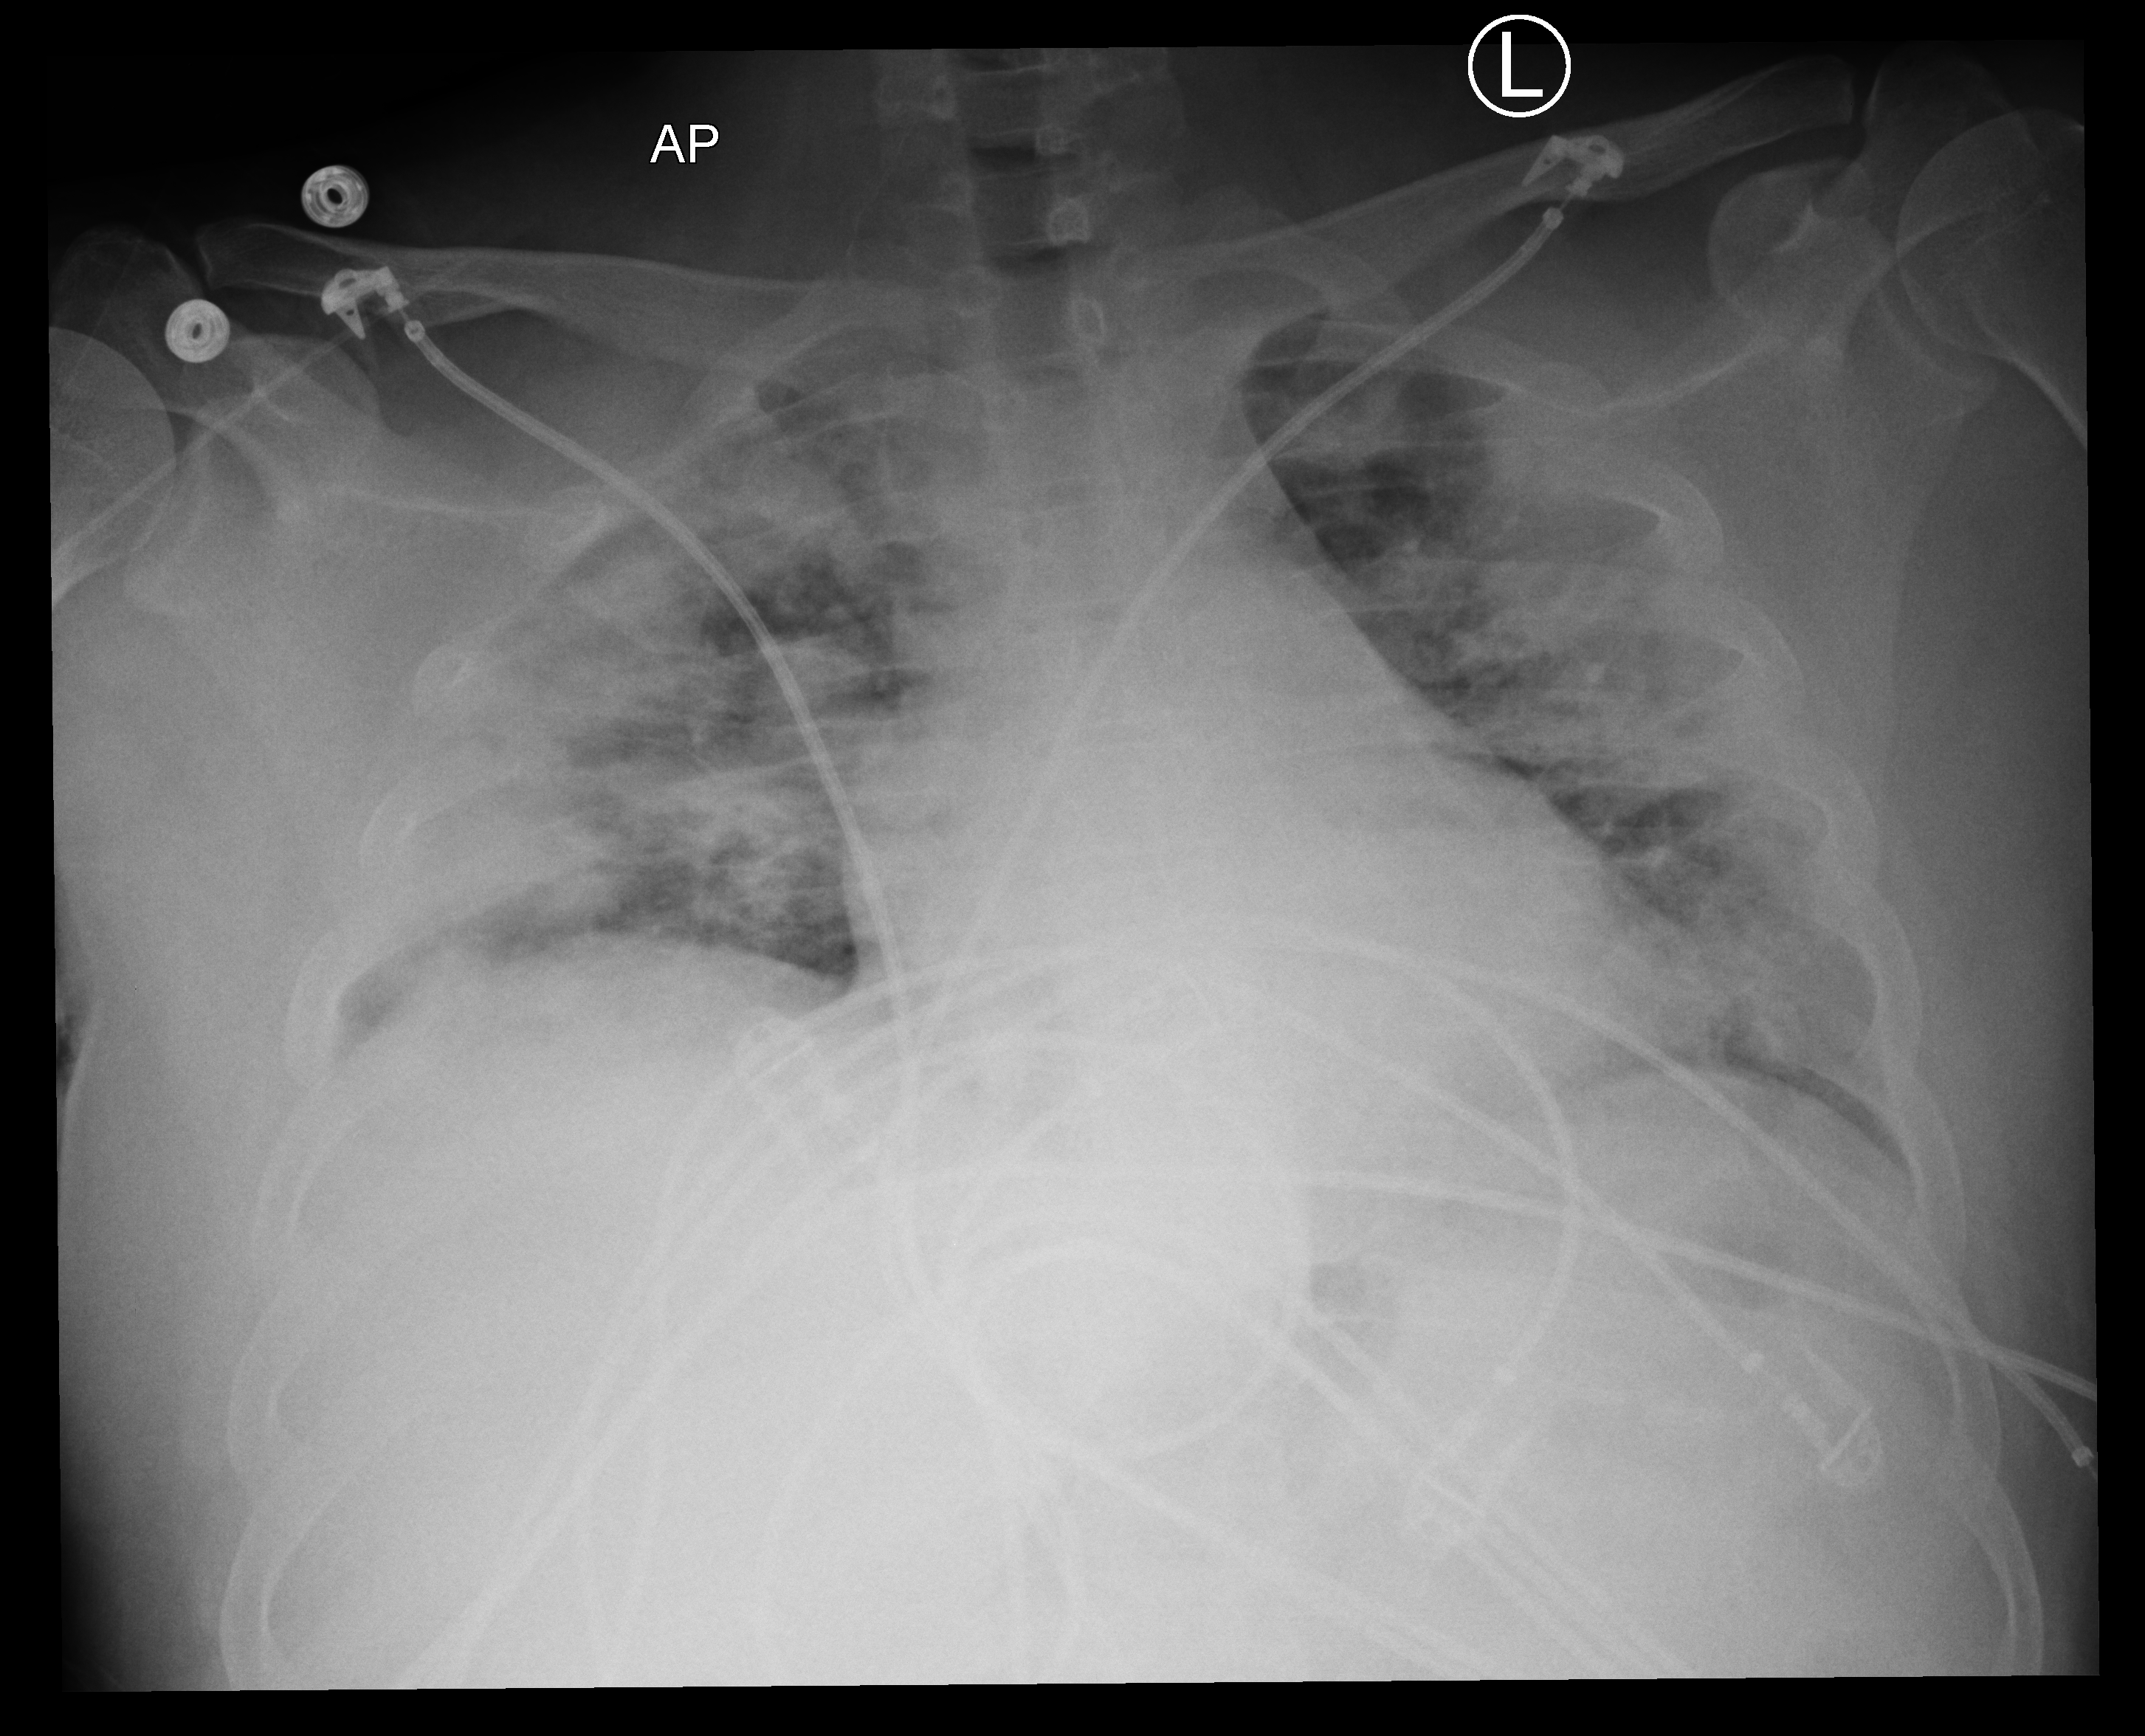
Chest X-ray (portable); anteroposterior (AP) projection. Patient hospitalised with COVID-19; male, aged 18–59 years.
Admission-level facts for this patient (not findings on this image; timing relative to this image not recorded):
- mechanically ventilated during this hospital stay: yes
- length of hospital stay: 44 days